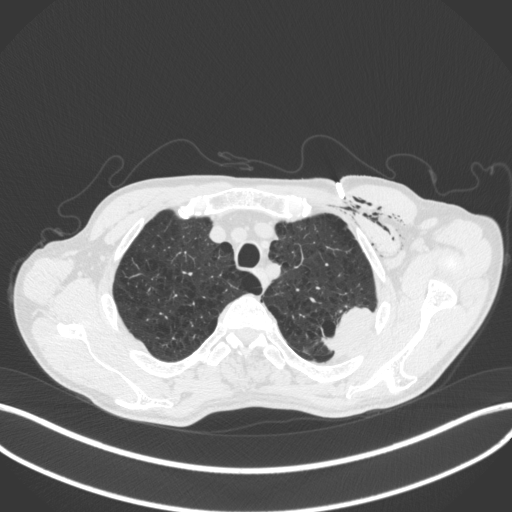
Chest CT, one axial slice; slice 346 of 416 in the series (ordered by position); 120 kVp; lung window (W 1500 / L -600 HU); 512 × 512 image matrix, field of view 400 × 400 mm. Patient: male, 58 years. Case-level facts recorded for this patient, not image findings: clinical TNM (as recorded): T3 N0 M0.
Outlined on this slice (bounding box drawn by a radiologist):
- lung tumour (recorded histology: adenocarcinoma): bounding box (x1, y1, x2, y2) in pixels: (316, 302, 379, 361)